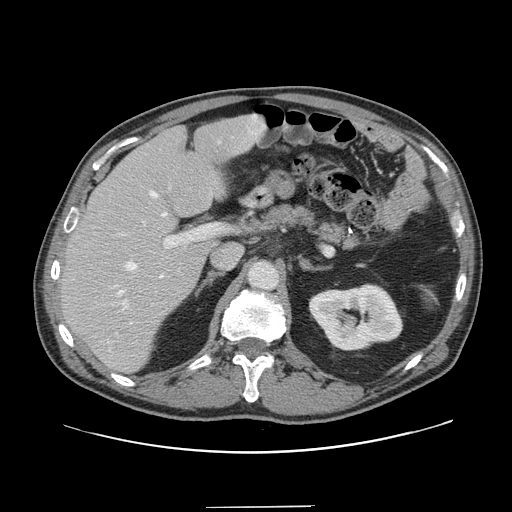
Contrast-enhanced abdominal CT, one axial slice. 120 kVp. Intravenous contrast given. Soft-tissue window (W 400 / L 40 HU). 2.5 mm slice thickness. 512 × 512 image matrix, field of view 397 × 397 mm. Male patient, age 64 years. Case-level facts recorded for this patient, not image findings: diagnosis: colorectal cancer liver metastases, imaged before liver resection; multiple liver metastases: yes; largest metastasis: 3.5 cm; disease in both lobes: yes.
Structures marked on this image (manually delineated by an expert):
- hepatic veins: bounding box <118,130,257,295> (left, top, right, bottom; pixels)
- liver: <61,116,264,372>
- planned liver remnant (the part of the liver to remain after resection): <62,116,264,372>
- portal vein (with intrahepatic branches): <119,223,218,310>